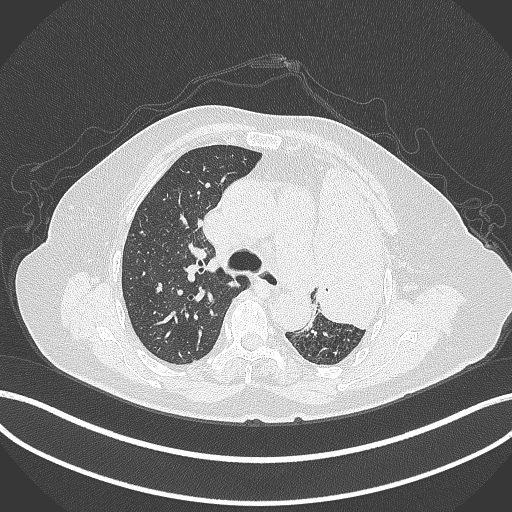
Chest CT, one axial slice. Reconstruction kernel B70f. Lung window (W 1500 / L -600 HU). 1 mm slice thickness. 512 × 512 image matrix, field of view 400 × 400 mm. Female patient, age 75 years. Case-level facts recorded for this patient, not image findings: clinical TNM (as recorded): T3 N3 M1.
Structures marked on this image (bounding box drawn by a radiologist):
- lung tumour (recorded histology: adenocarcinoma): bounding box [x1, y1, x2, y2] px = [309, 154, 390, 330]